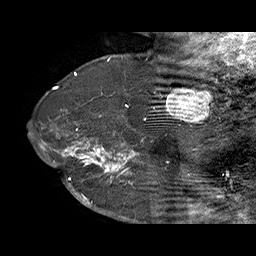
Breast MRI (dynamic contrast-enhanced), one sagittal slice. Slice 50 of 70 in the series (ordered by position). Dynamic contrast-enhanced series, time point 2 of 6 at this slice position (early post-contrast). 1.5 T. TE 4.5 ms, TR 32.4 ms. 256 × 256 image matrix. Female patient. Case-level facts recorded for this patient, not image findings: setting: breast cancer imaged before/during neoadjuvant chemotherapy; receptor status: HR-positive, HER2-negative.
Outlined on this slice (semi-automatic segmentation, software-assisted and operator-edited):
- analysis volume of interest (the breast-tissue region the enhancement analysis was run in; not a lesion): box from (x=71, y=128) to (x=159, y=202) px
- tumour enhancement mask (voxels above the 100 % enhancement threshold inside the analysis volume of interest): (x=71, y=129)–(x=143, y=202)